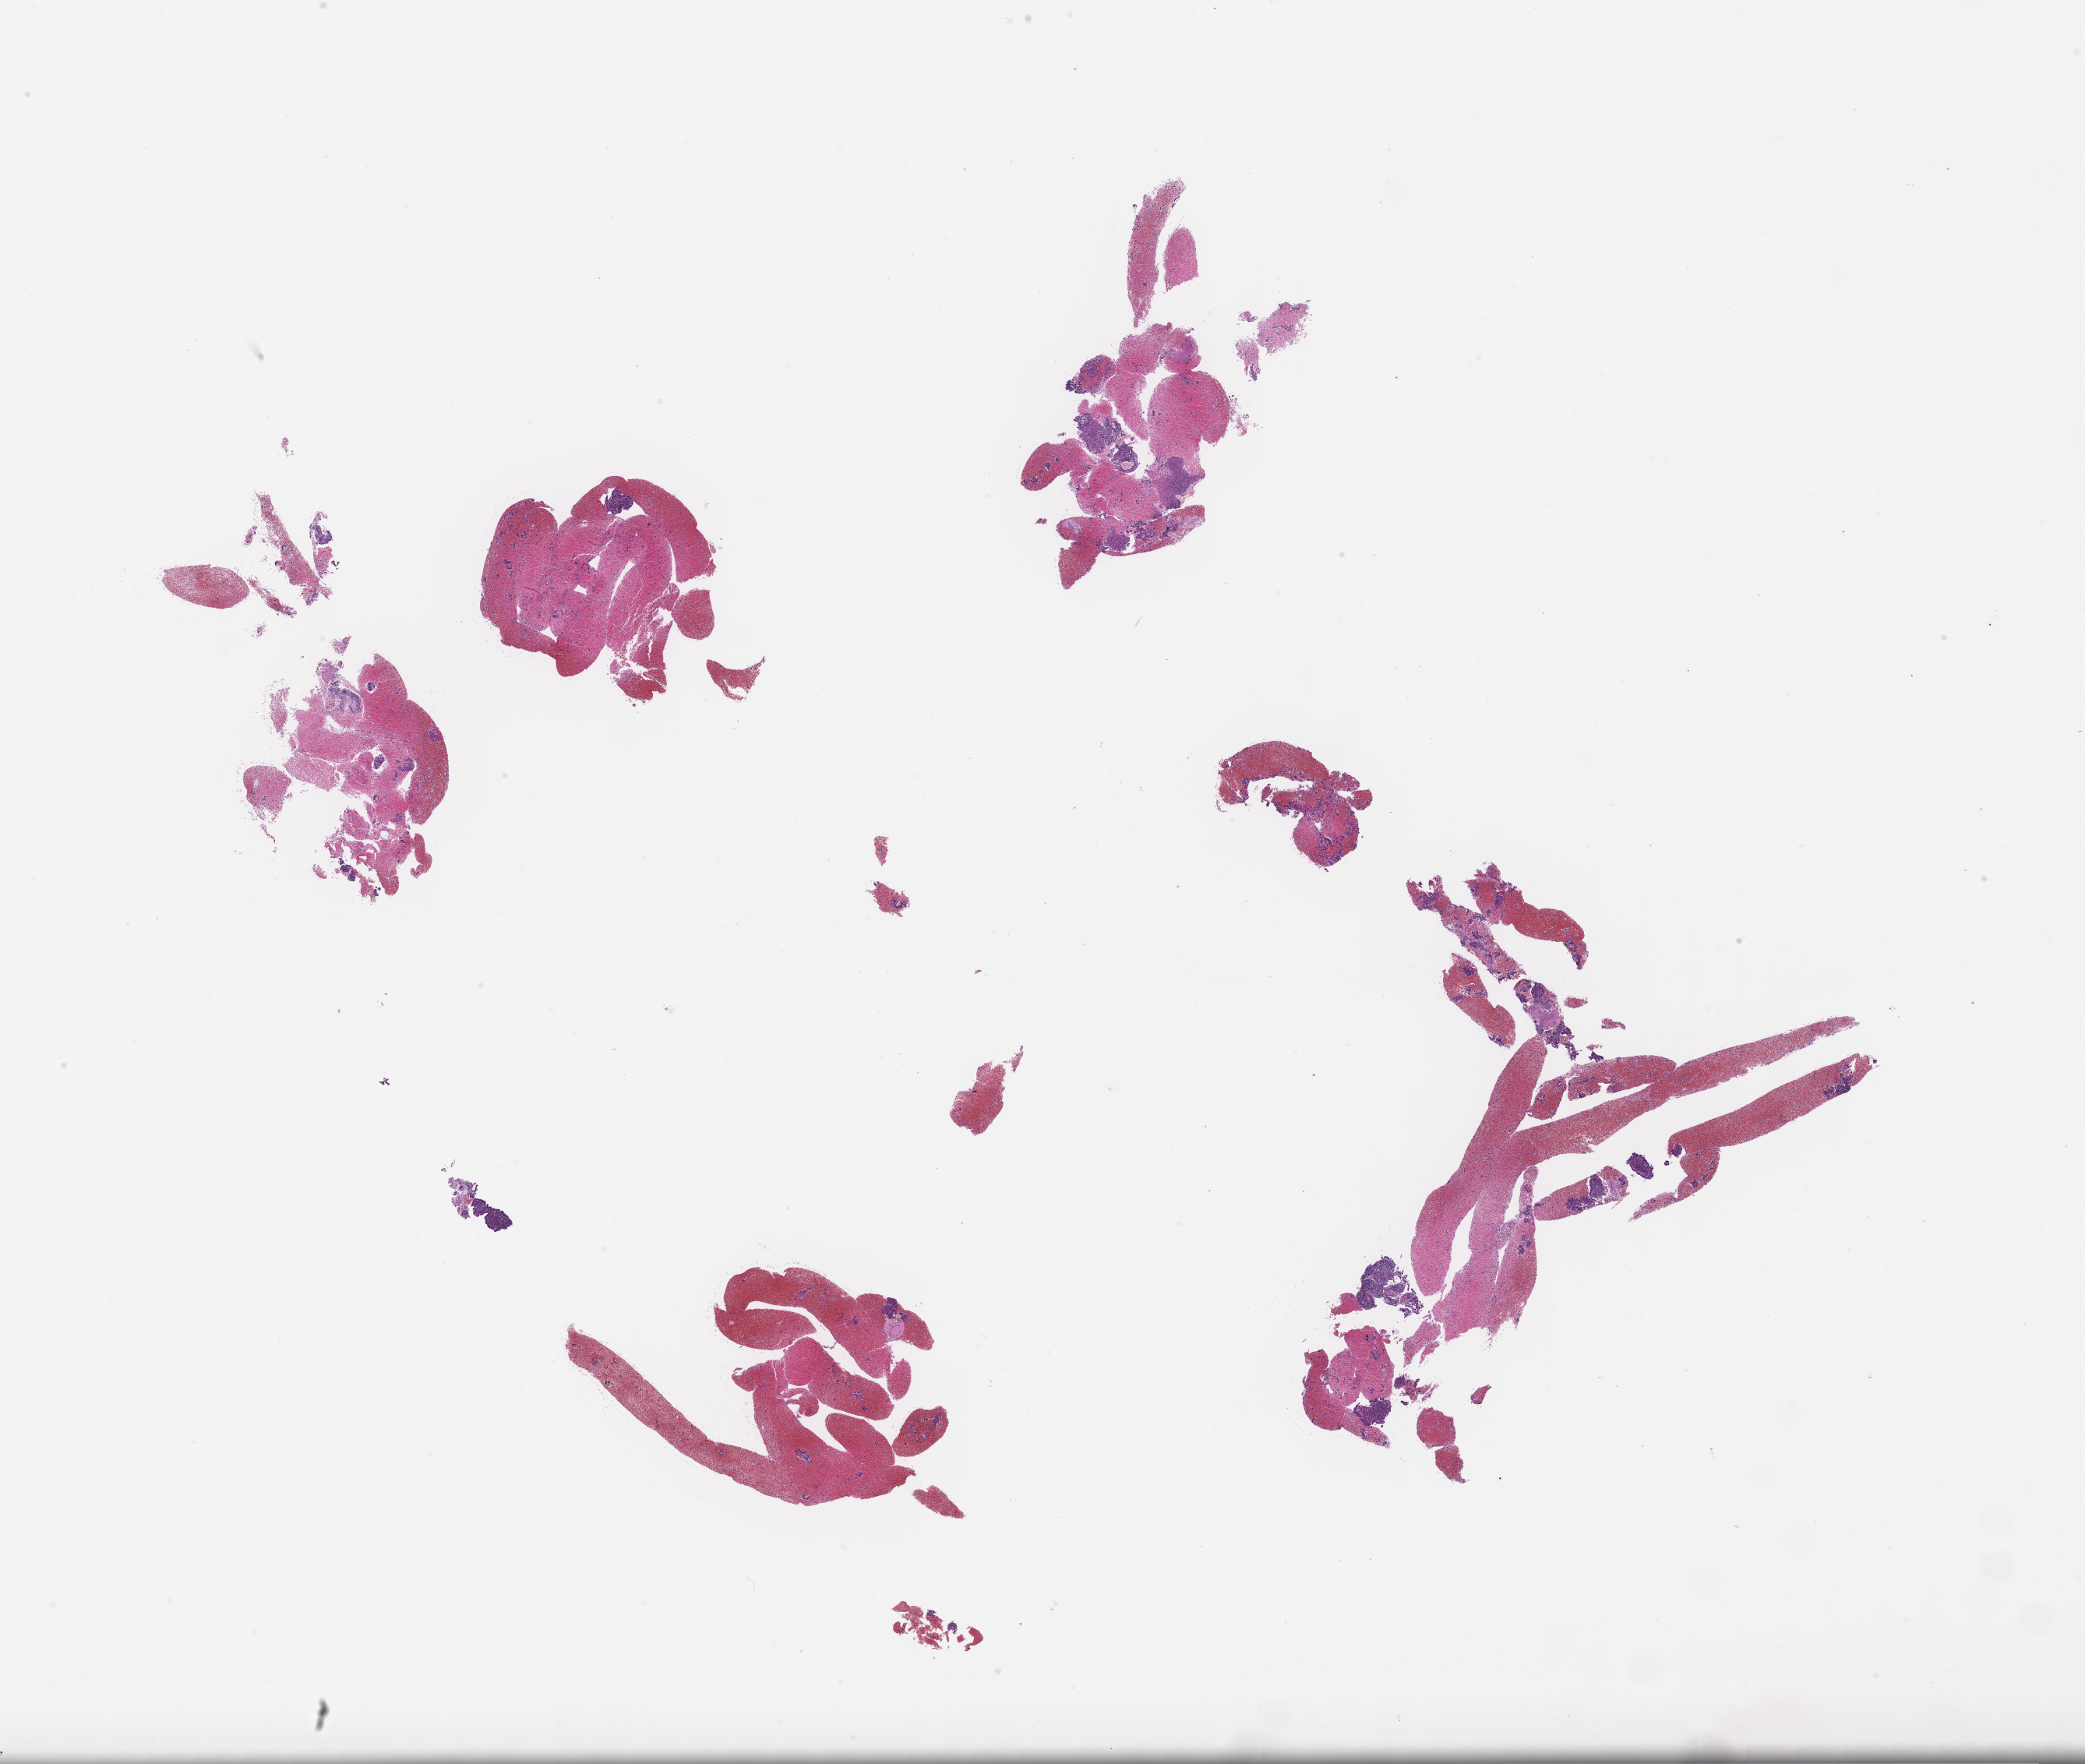
Hematoxylin and eosin (H&E) whole-slide image, a low-resolution overview of the entire scanned area, about 21.6 x 18.3 mm, formalin-fixed paraffin-embedded section, site: lung. Patient sex: male.
This section: primary tumour tissue. Diagnosis: Non-Small Cell Lung Carcinoma.